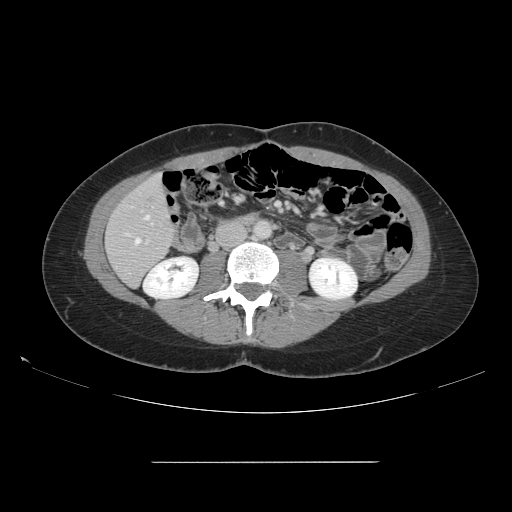
Contrast-enhanced abdominal CT, one axial slice; slice 44 of 151 in the series (ordered by position); 120 kVp; intravenous contrast given; soft-tissue window (W 400 / L 40 HU); 2.5 mm slice thickness; 512 × 512 image matrix, field of view 421 × 421 mm. Female patient, age 46 years. Case-level facts recorded for this patient, not image findings: diagnosis: colorectal cancer liver metastases, imaged before liver resection; multiple liver metastases: yes; largest metastasis: 3 cm; disease in both lobes: yes.
Annotated regions visible in this slice (expert manual segmentation):
- hepatic veins: bounding box (x1, y1, x2, y2) in pixels: (135, 215, 149, 243)
- liver: (106, 176, 176, 286)
- planned liver remnant (the part of the liver to remain after resection): (106, 176, 175, 286)